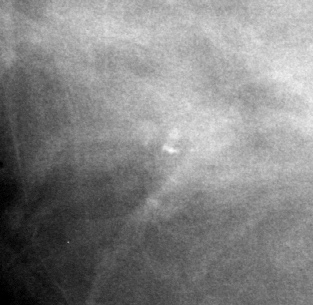
Cropped region of a digitized screen-film mammogram centred on a radiologist-marked abnormality; right breast; CC view; BI-RADS breast density category 3 (scale 1–4).
- Calcifications, morphology amorphous, distribution clustered; BI-RADS assessment category 4; pathology (as recorded): benign.